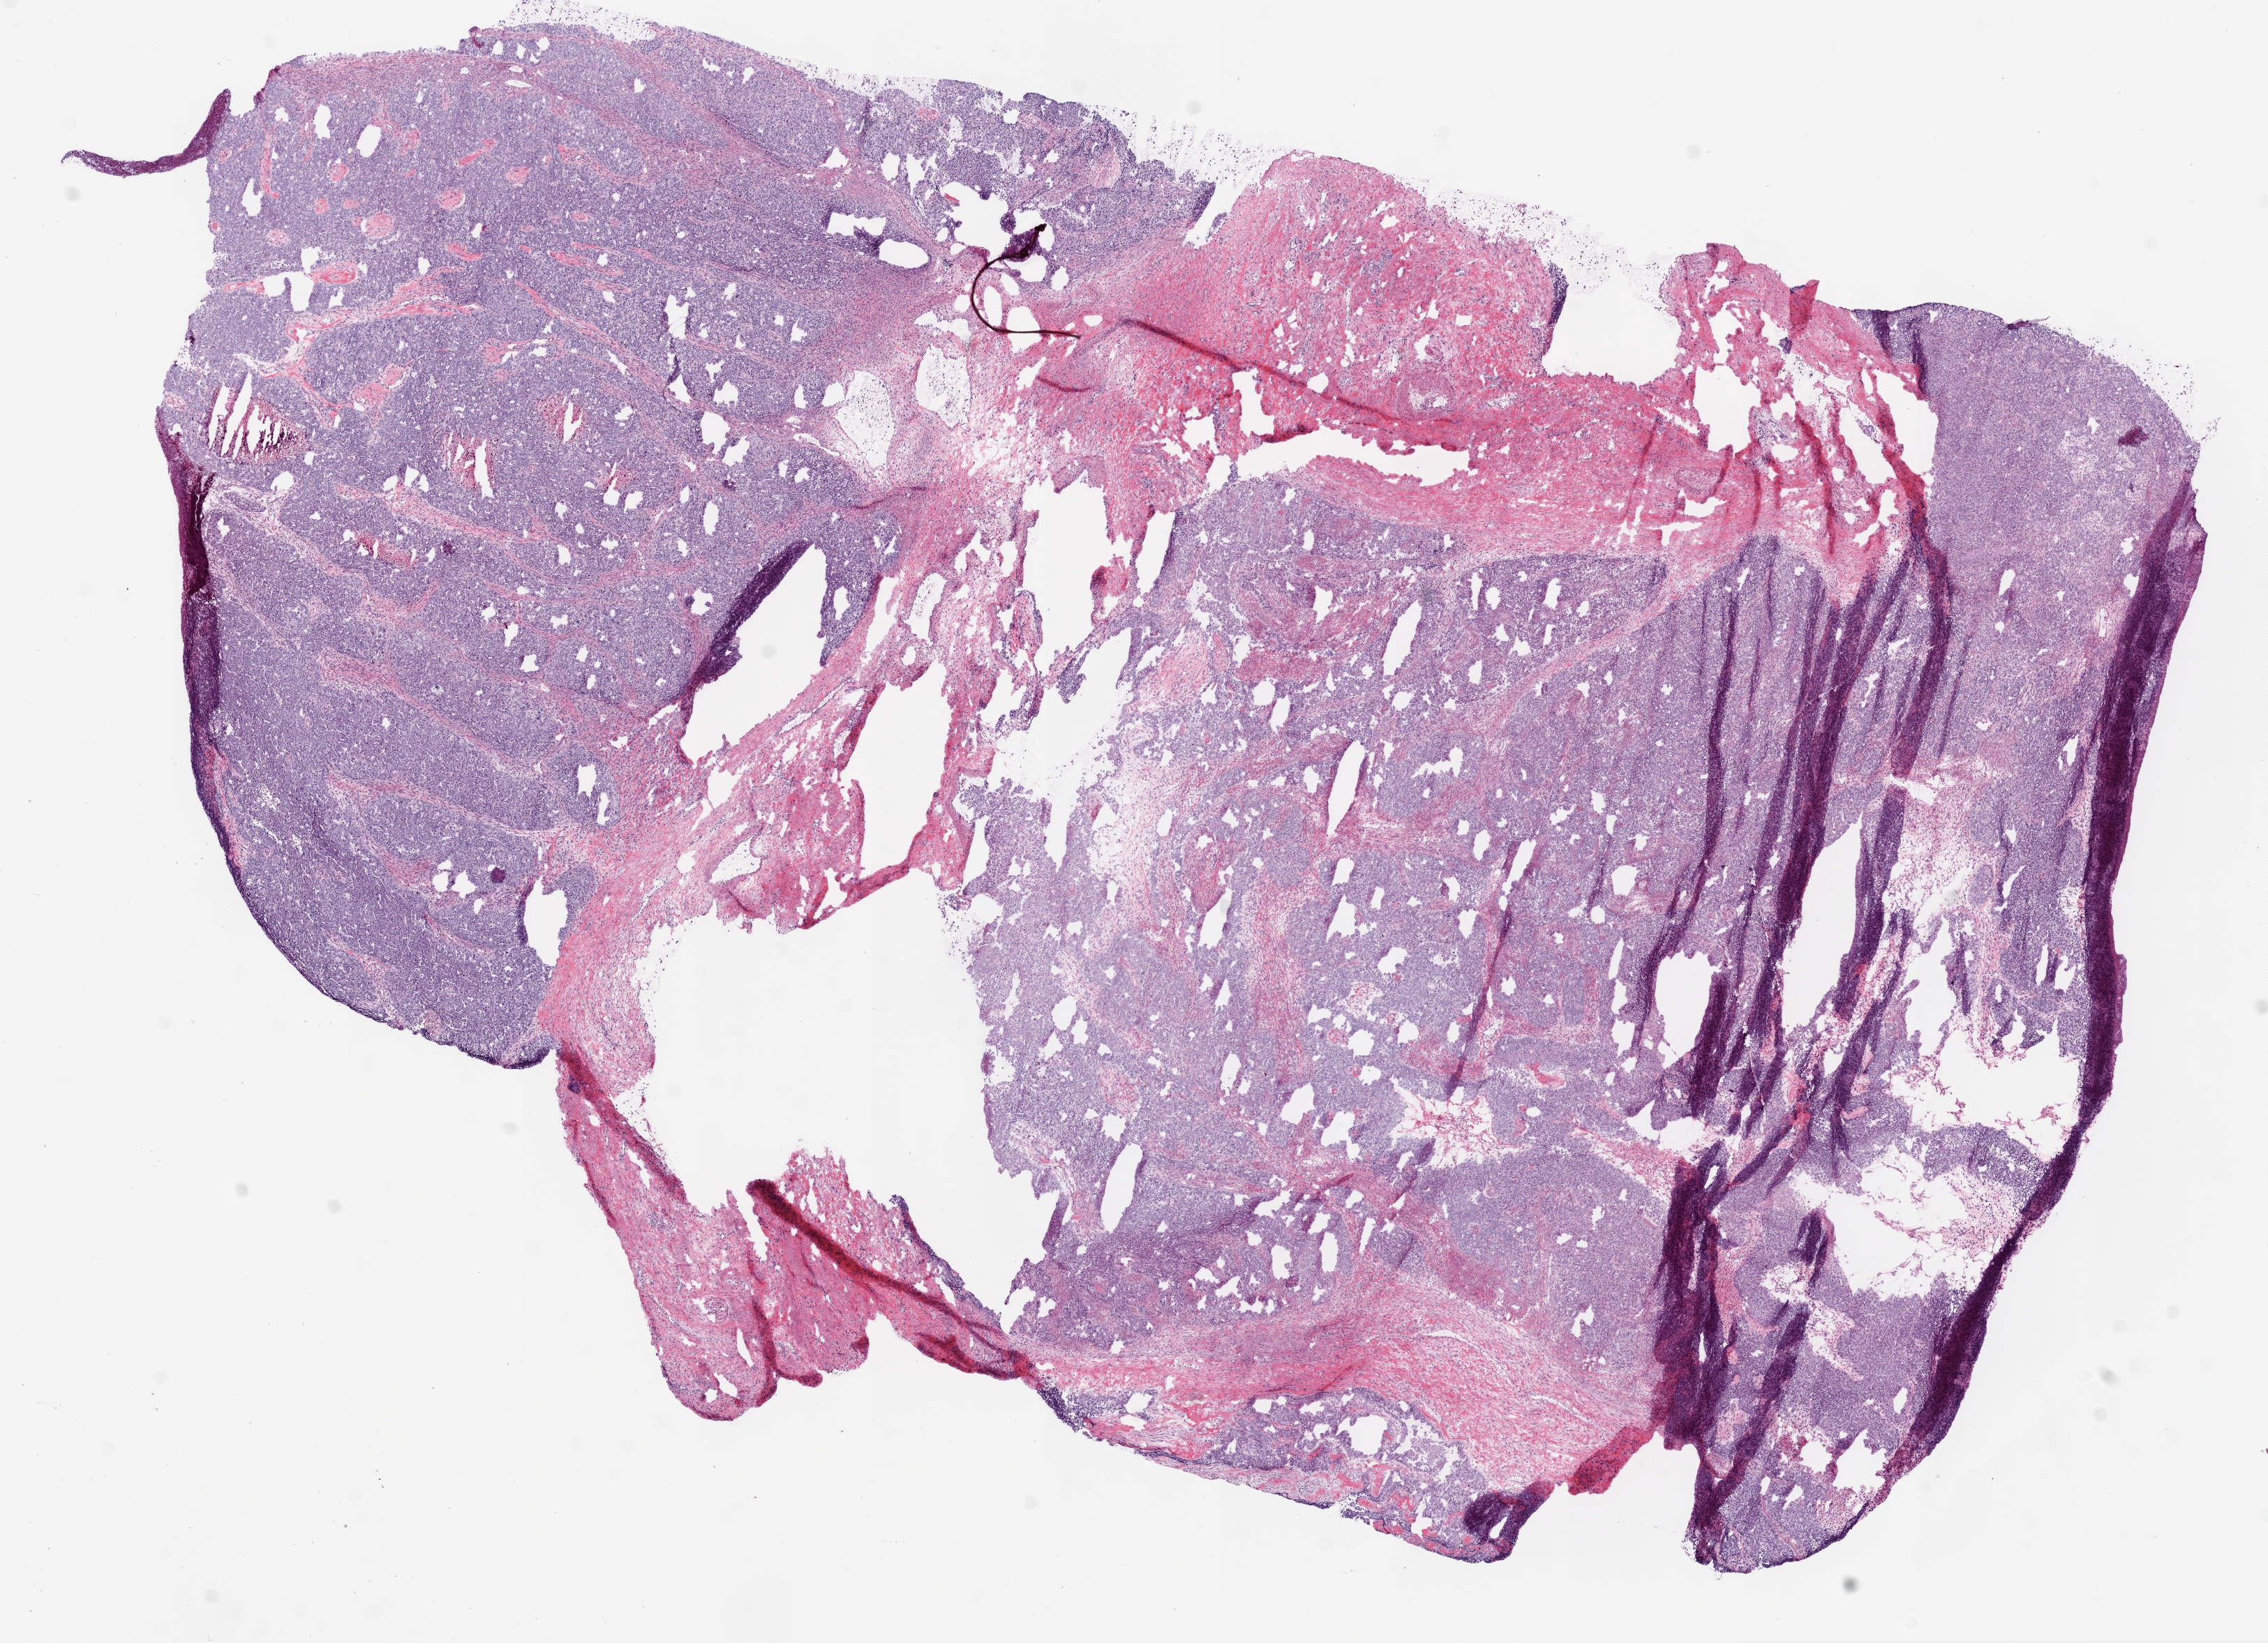
Digitized Hematoxylin and eosin (H&E) stained tissue section (whole slide), a low-resolution overview of the entire scanned area, about 13.0 x 9.4 mm, frozen section from the bottom of the tissue portion, primary tumour sample from the ovary. Patient: female, age at initial diagnosis 64 years. Histologic grade: G3 (poorly differentiated). Composition of this section per pathologist review: tumour cells 70%, tumour nuclei 75%, normal cells 0%, stromal cells 25%, necrosis 5%.
FIGO stage: IIIC. Diagnosis: Serous cystadenocarcinoma, NOS.